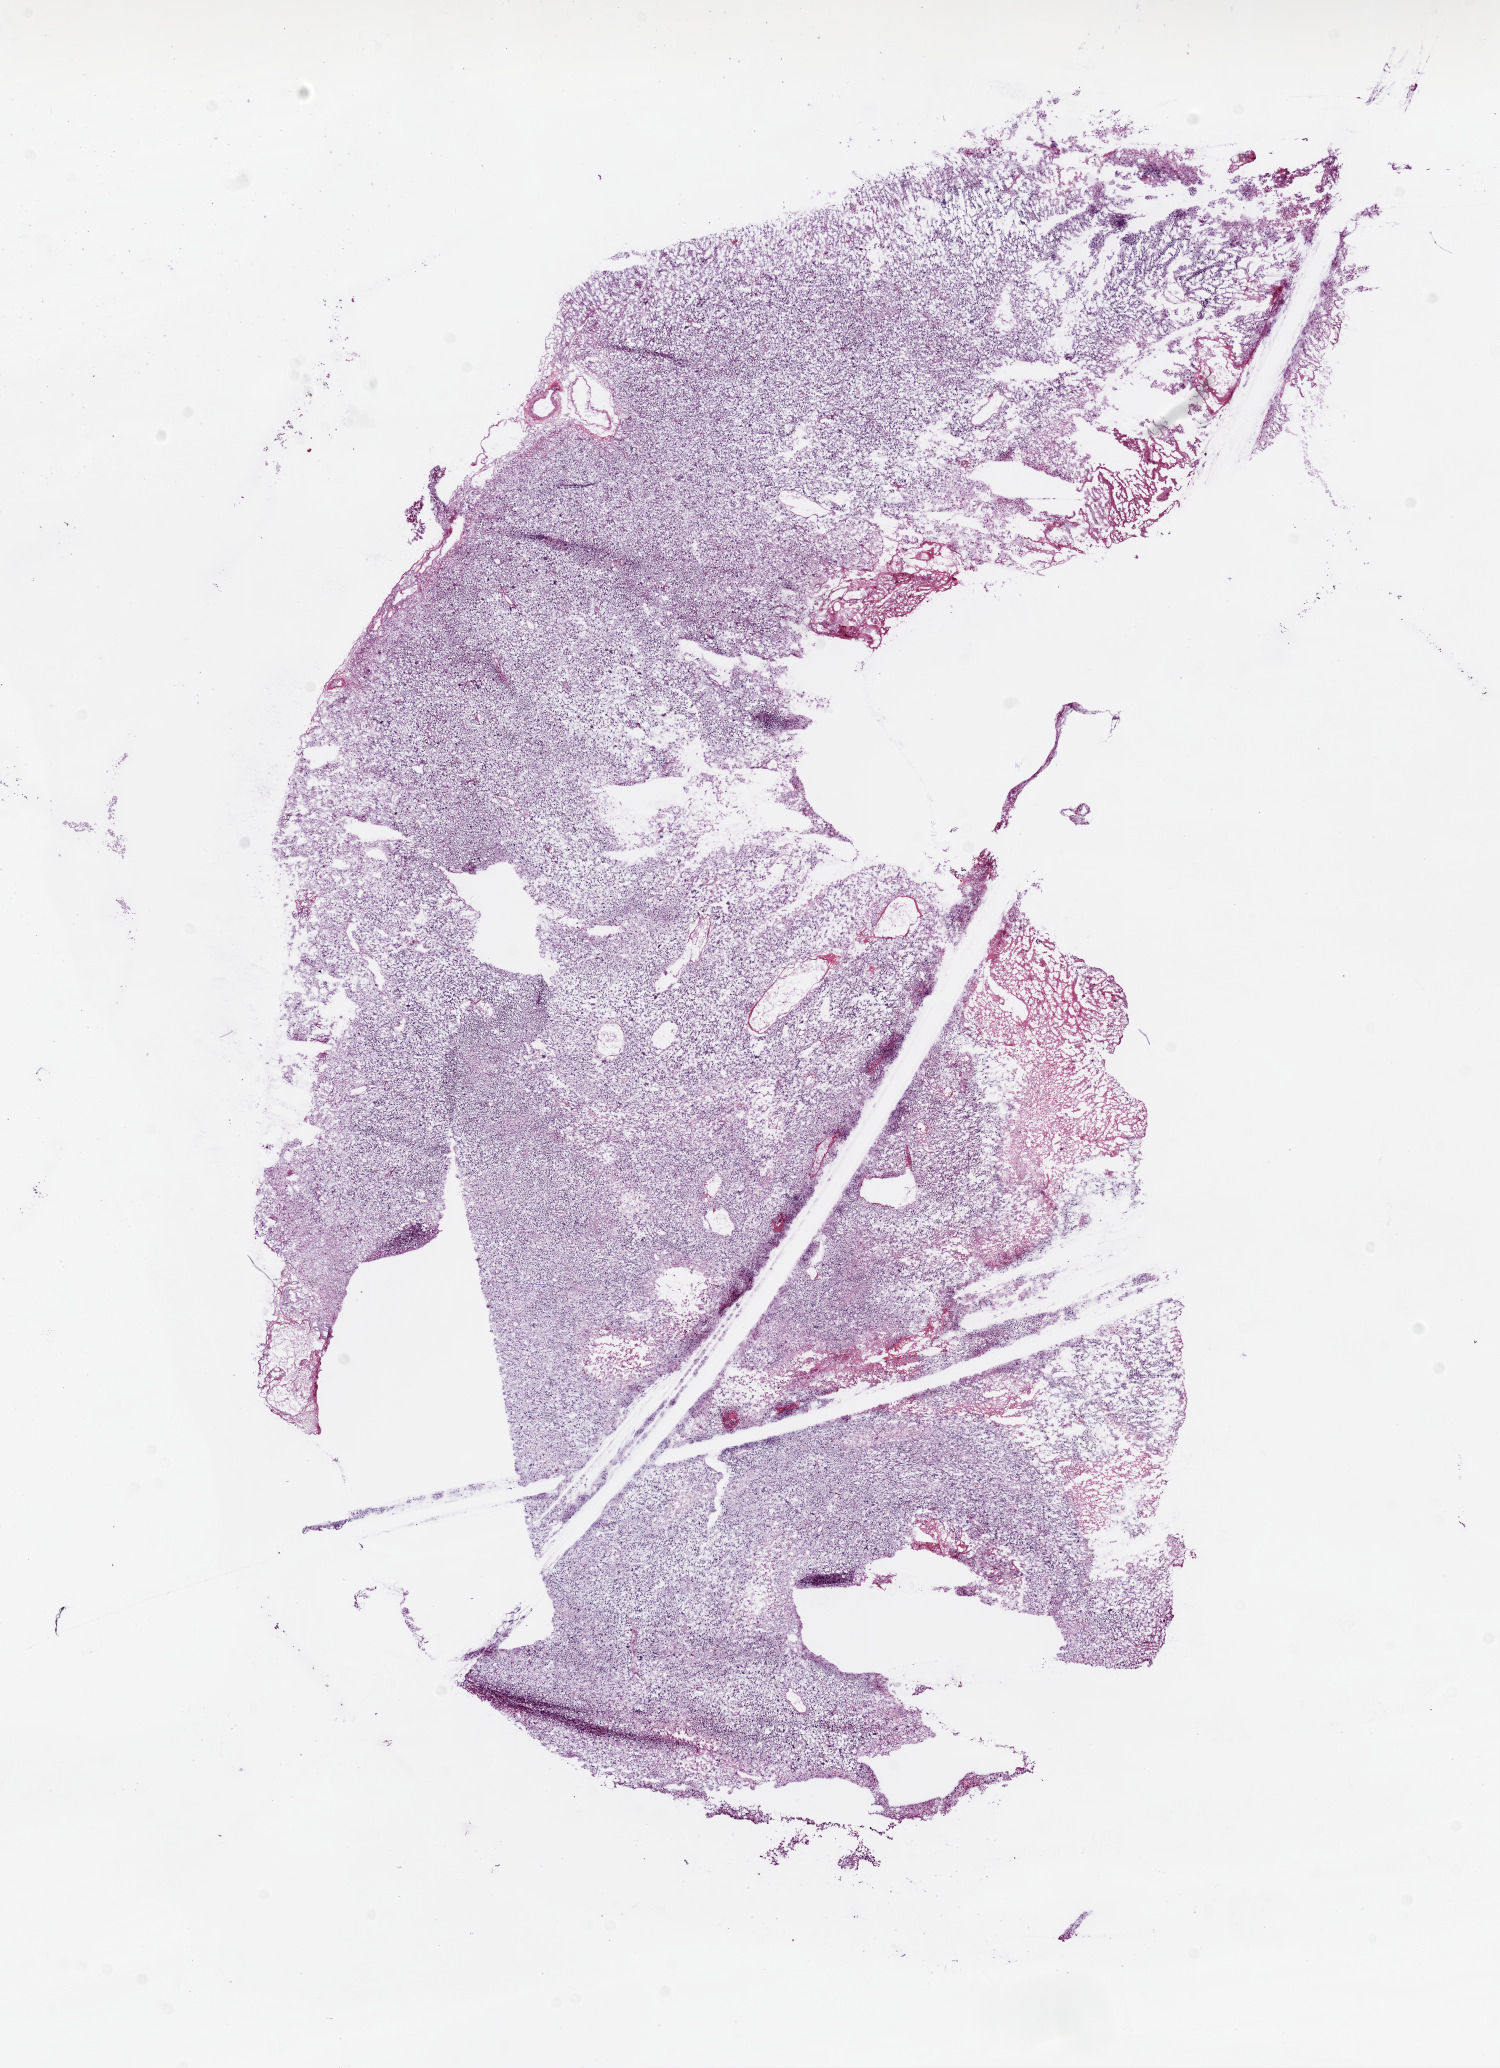
Digitized Hematoxylin and eosin (H&E) stained tissue section (whole slide) — whole scanned area (about 12.0 x 16.6 mm) shown as a low-resolution overview; frozen section from the bottom of the tissue portion; recurrent tumour sample from the brain. Female, age 60 years at initial diagnosis. Pathologist review of this section (percent, as recorded): tumour cells 80%, tumour nuclei 95%, normal cells 0%, stromal cells 0%, necrosis 20%.
This section: recurrent tumour. Patient diagnosis: Glioblastoma.